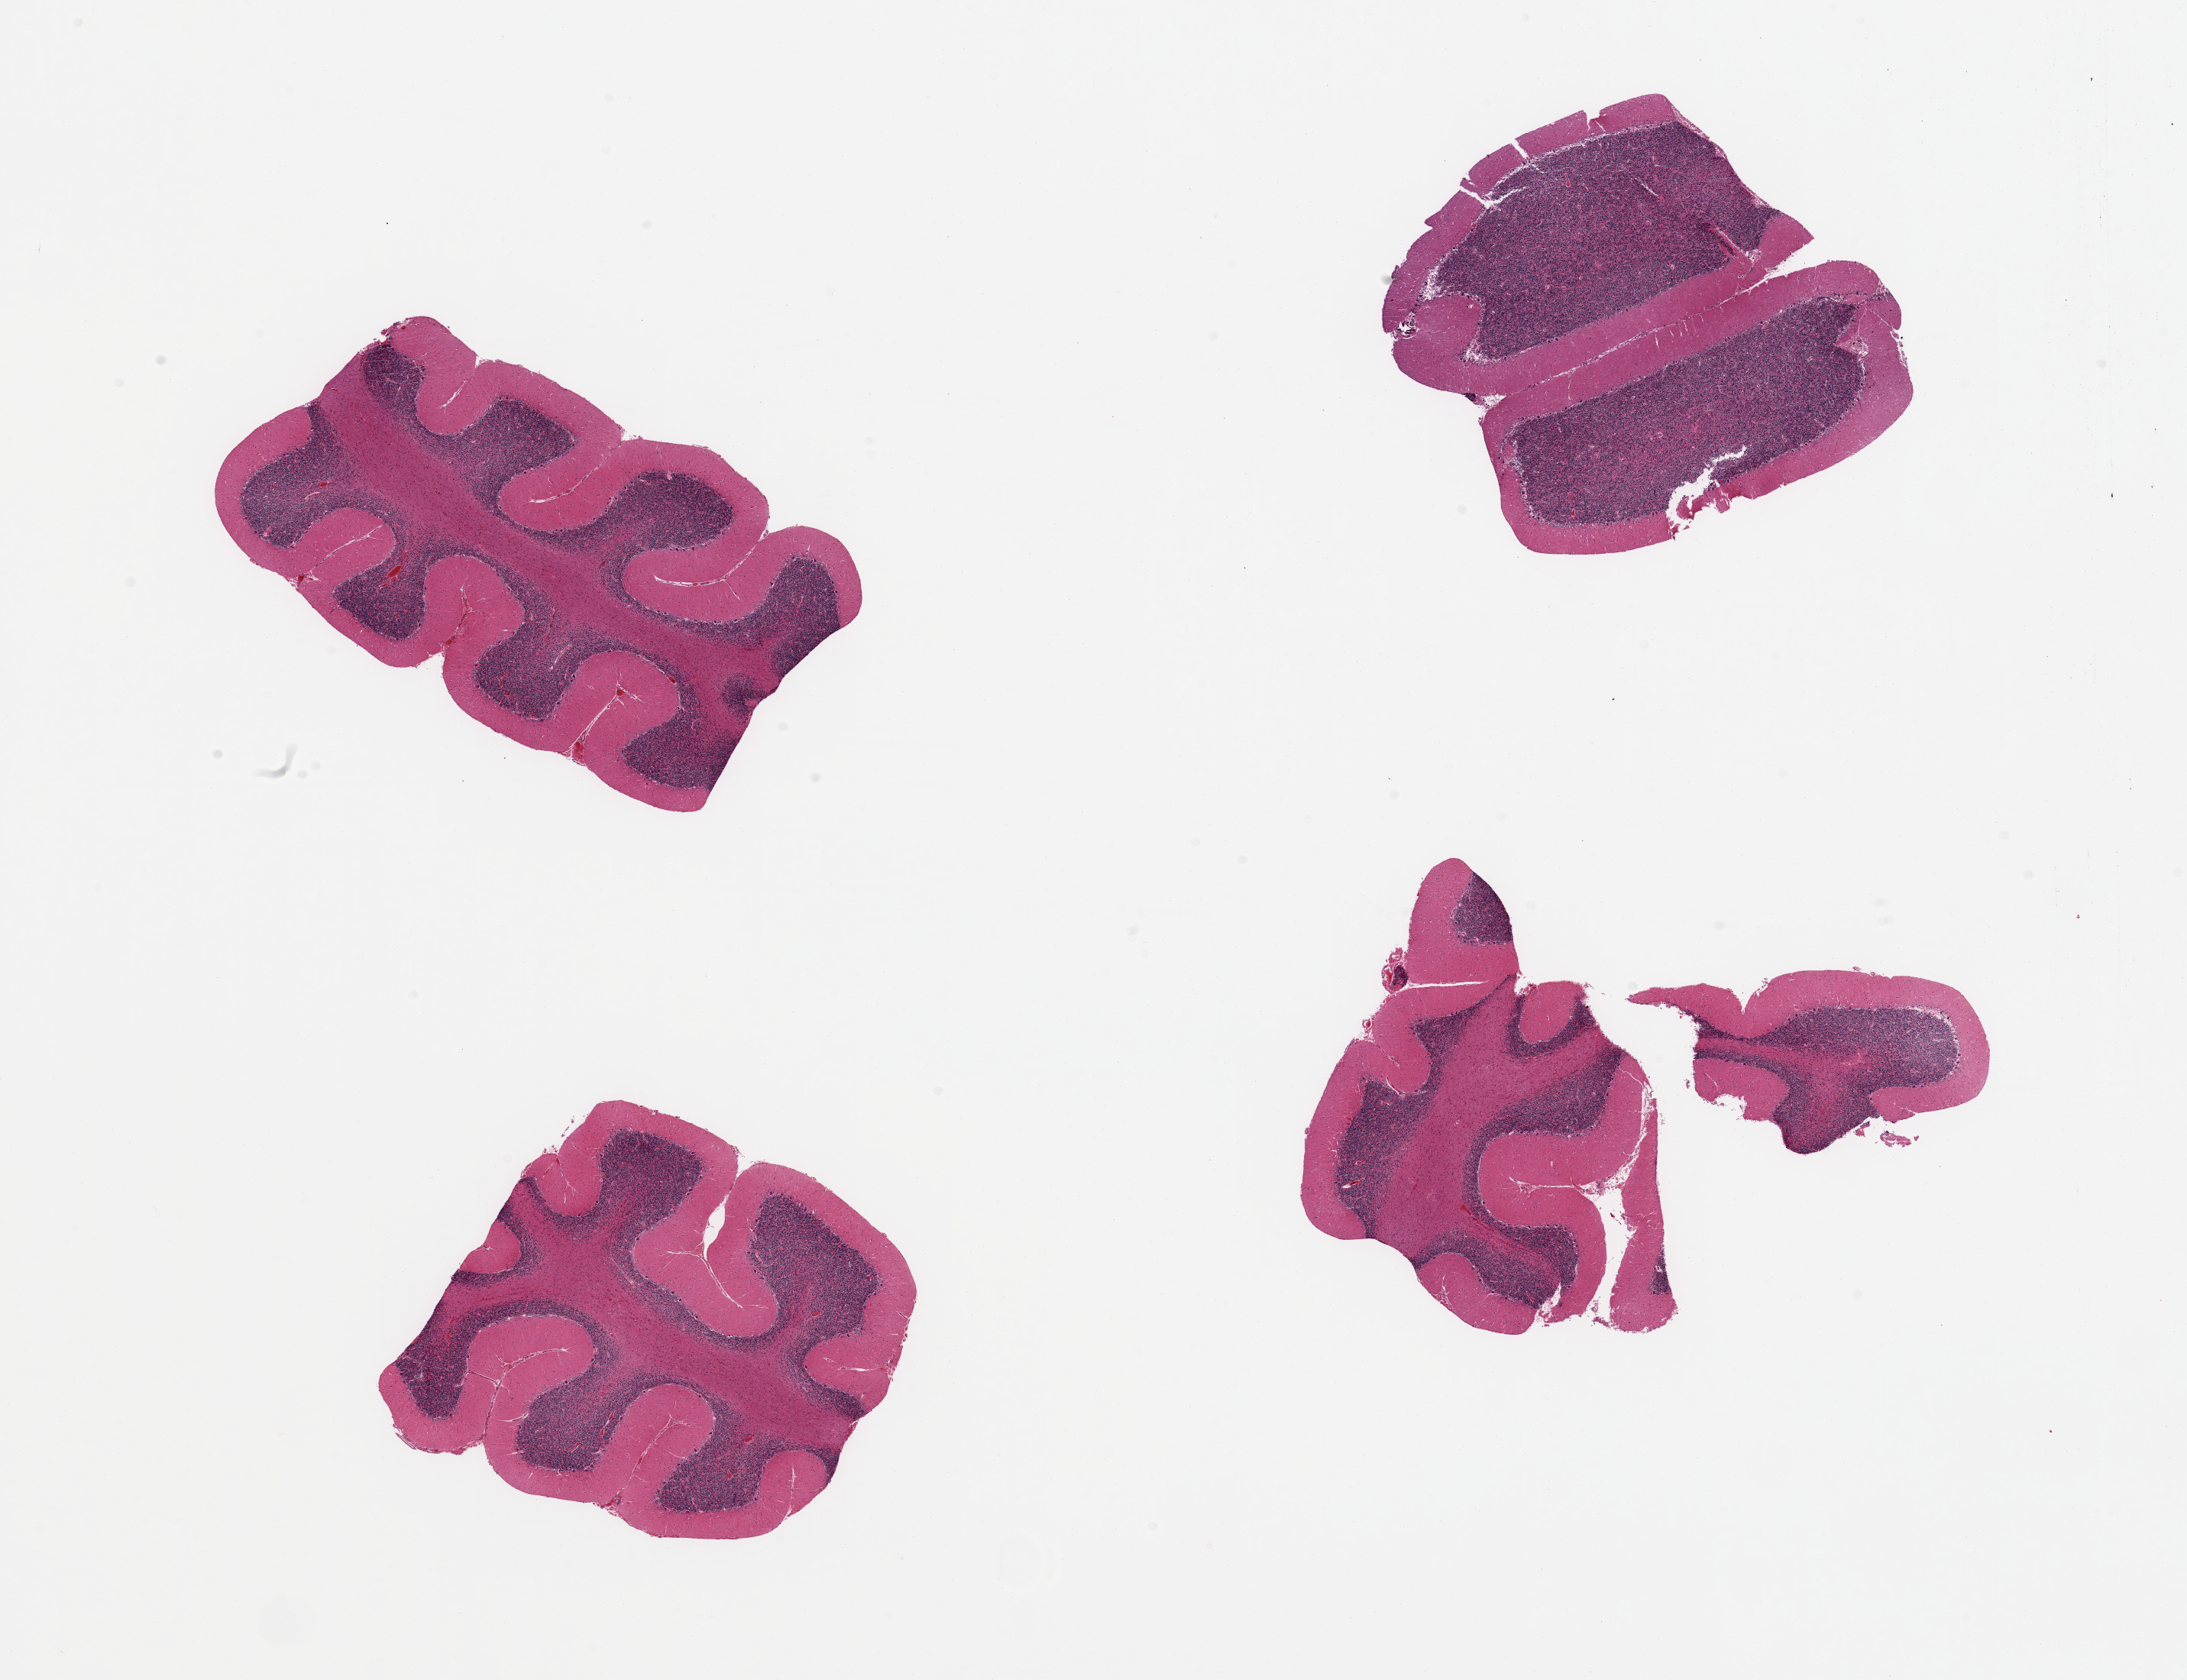
Whole-slide image, haematoxylin and eosin stain — a low-resolution overview of the entire scanned area, about 22.6 x 17.4 mm. PAXgene-fixed paraffin-embedded (PFPE) section. Section of cerebellum (target tissue). Donor tissue sample. Donor: female.
Reviewer comment on this tissue sample: 4 pieces; Purkinje cells well visualized.